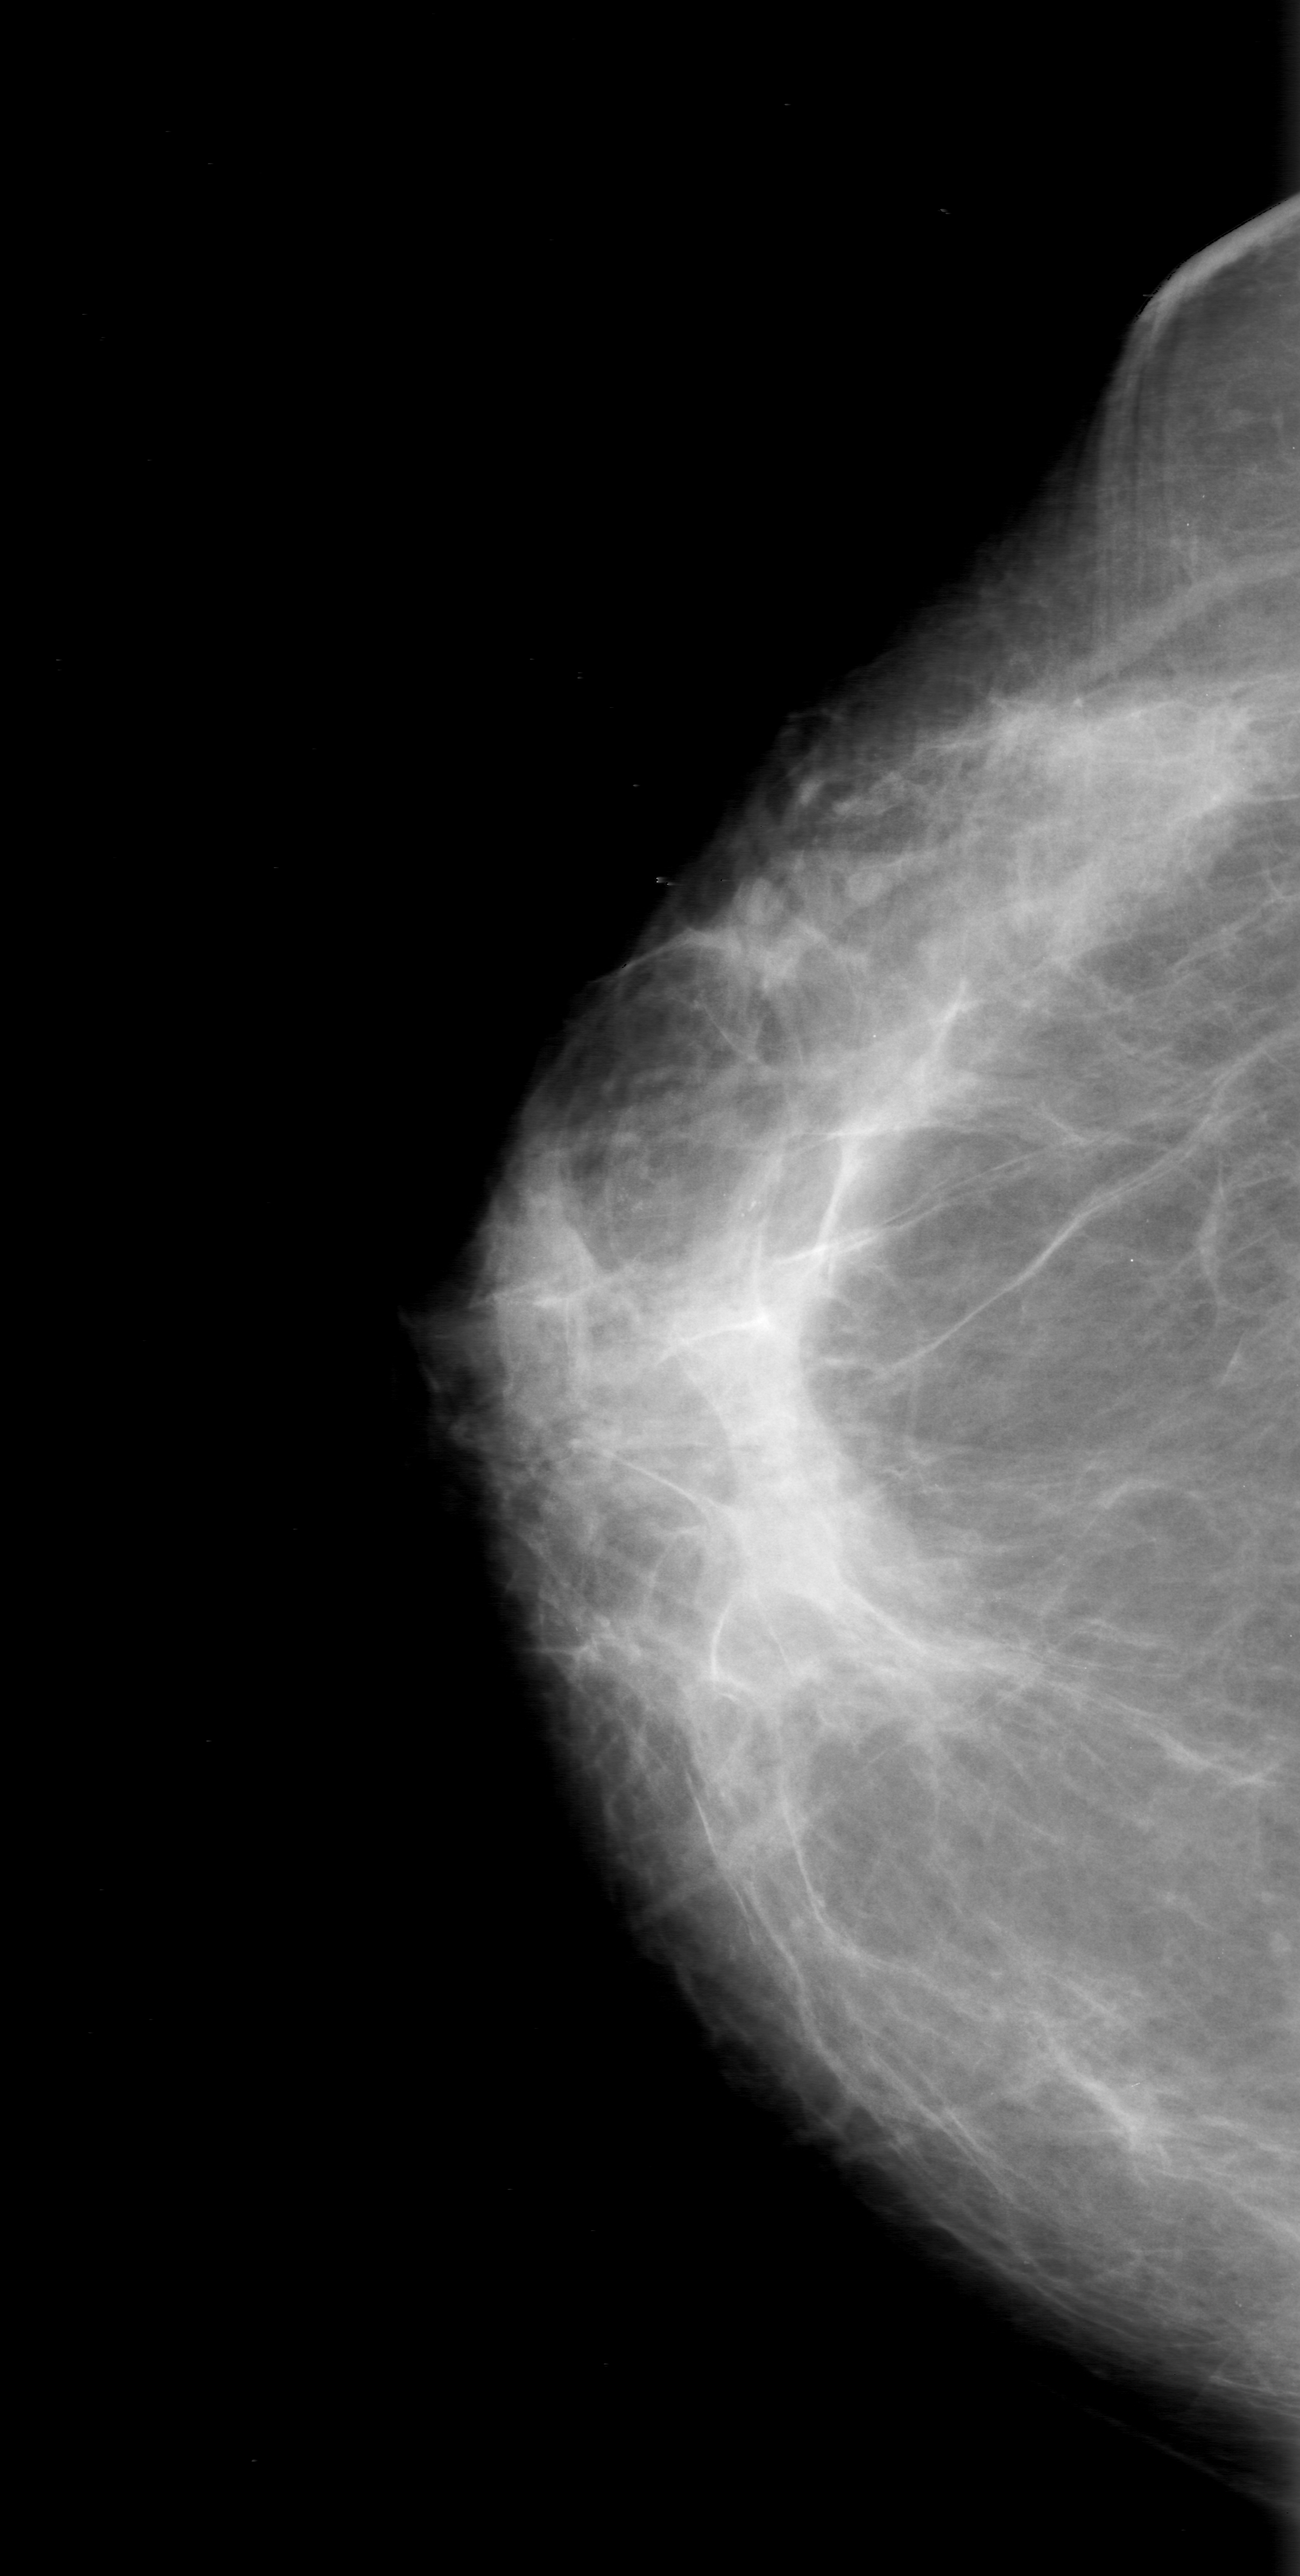
Scanned film-screen mammogram, right breast, CC view, BI-RADS breast density category 2 (scale 1–4).
Calcifications, morphology amorphous, distribution clustered; BI-RADS assessment category 0; pathology result (as recorded, not read from the image): benign.